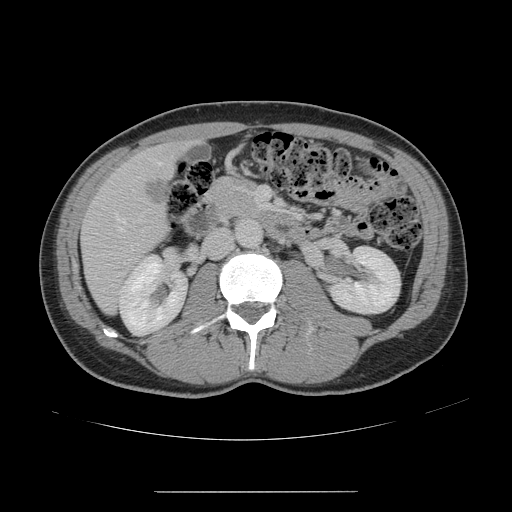
Contrast-enhanced abdominal CT, one axial slice; position 57 of 178 along the scan axis; 120 kVp; intravenous contrast given; soft-tissue window (W 400 / L 40 HU); 2.5 mm slice thickness; 512 × 512 image matrix, field of view 401 × 401 mm. Male patient, age 53 years. Case-level facts recorded for this patient, not image findings: diagnosis: colorectal cancer liver metastases, imaged before liver resection; multiple liver metastases: yes; largest metastasis: 2.4 cm; disease in both lobes: no.
Structures marked on this image (expert manual segmentation):
- hepatic veins: bounding box [x1, y1, x2, y2] px = [110, 161, 161, 248]
- liver: [82, 144, 185, 311]
- portal vein (with intrahepatic branches): [255, 187, 267, 208]
- liver metastasis: [142, 180, 167, 205]